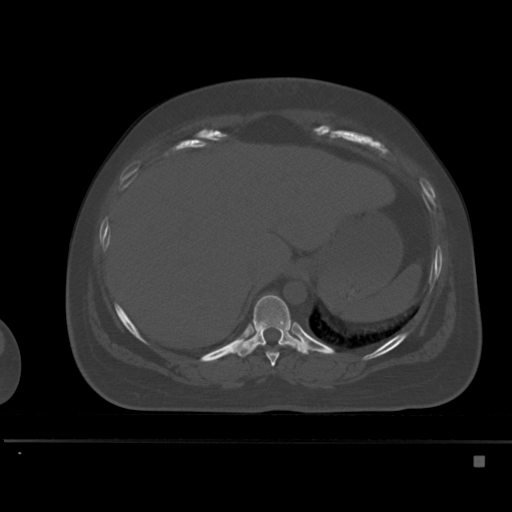
CT including the spine, one axial slice. Slice 253 of 495 in the series (ordered by position). Bone window (W 1800 / L 400 HU). 1.5 mm slice thickness. 512 × 512 image matrix, field of view 404 × 404 mm. Patient: female, 33 years. From the clinical record (not read from this slice): primary cancer: breast; vertebrae with lytic lesions (as recorded): T1.
Annotated regions visible in this slice (semi-automatically segmented with operator editing):
- T10 vertebra: bounding box (x1, y1, x2, y2) in pixels: (235, 294, 310, 357)
- T9 vertebra: (266, 344, 284, 366)